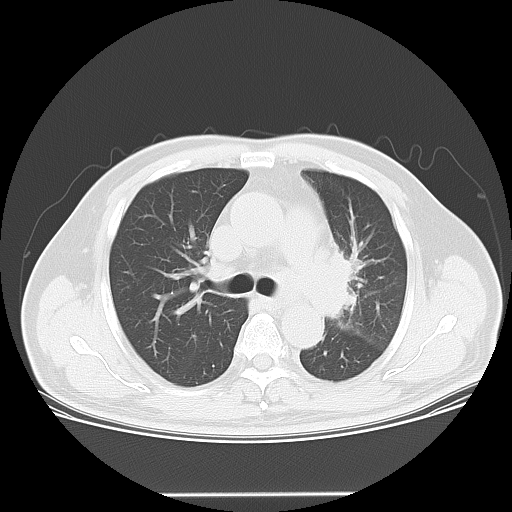
Chest CT, one axial slice. Position 37 of 55 along the scan axis. Reconstruction kernel LUNG. Lung window (W 1500 / L -600 HU). 512 × 512 image matrix. Patient: male, 61 years. Case-level facts recorded for this patient, not image findings: clinical TNM (as recorded): T3 N1 M1.
Annotated regions visible in this slice (rectangle marked by the reading radiologist):
- lung tumour (recorded histology: small cell carcinoma): box from (x=316, y=236) to (x=365, y=330) px